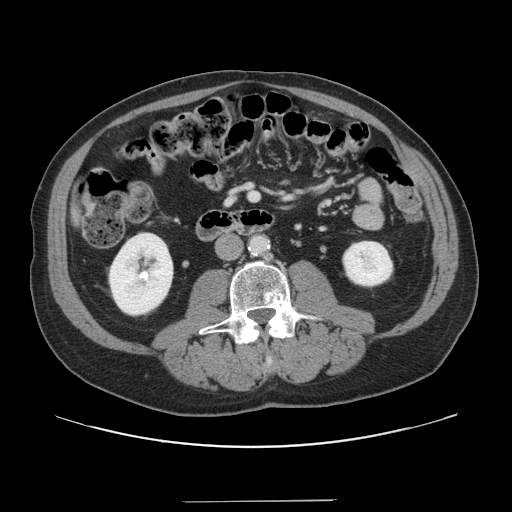
Contrast-enhanced abdominal CT, one axial slice. Position 33 of 151 along the scan axis. 120 kVp. Intravenous contrast given. Soft-tissue window (W 400 / L 40 HU). 2.5 mm slice thickness. 512 × 512 image matrix, field of view 399 × 399 mm. Male patient, age 63 years. Case-level facts recorded for this patient, not image findings: diagnosis: colorectal cancer liver metastases, imaged before liver resection; multiple liver metastases: no; largest metastasis: 2.1 cm; chemotherapy before resection: no.
Annotated regions visible in this slice (expert manual segmentation):
- liver: bounding box [x1, y1, x2, y2] px = [77, 220, 79, 222]
- portal vein (with intrahepatic branches): [250, 193, 258, 200]